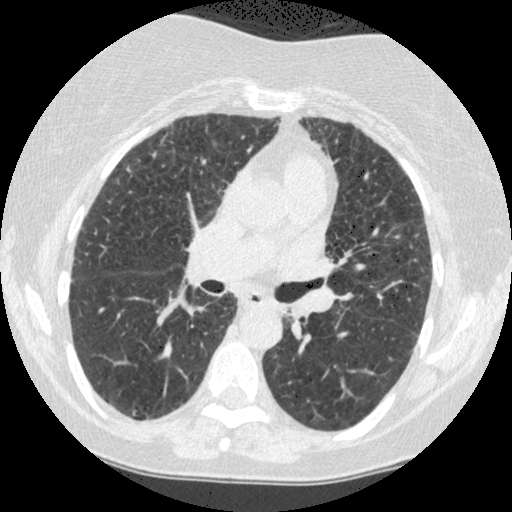
Chest CT (low-dose screening protocol), one axial image; baseline screening round; lung window (W 1500 / L -600 HU); 1.25 mm slice thickness; 120 kVp; 512 × 512 image matrix, field of view 310 × 310 mm. Female, age 60 years at enrolment.
Lesion marked by an expert reader, box from (x=274, y=296) to (x=313, y=339) px. The screening reader recorded 2 non-calcified nodules or masses ≥4 mm on this exam (right lower lobe, left lower lobe); which of them this box marks is not recorded. Later outcome: lung cancer diagnosed 794 days after this screen — small cell carcinoma, NOS, left lower lobe, undifferentiated (G4), stage IV (AJCC 6th edition), 69 mm at pathology.